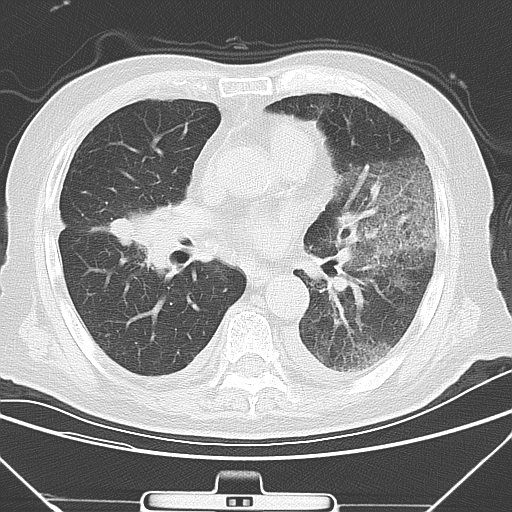
Chest CT, one axial slice; position 17 of 43 along the scan axis; lung window (W 1500 / L -600 HU); 5 mm slice thickness; 512 × 512 image matrix. Male patient, age 85 years. Case-level facts recorded for this patient, not image findings: clinical TNM (as recorded): T4 N3 M2.
Structures marked on this image (bounding box drawn by a radiologist):
- lung tumour (recorded histology: squamous cell carcinoma): bounding box [x1, y1, x2, y2] px = [95, 201, 192, 278]